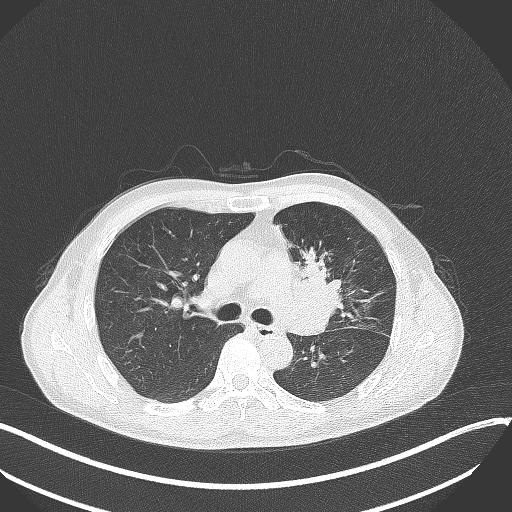
Chest CT, one axial slice. Slice 211 of 411 in the series (ordered by position). Reconstruction kernel B70f. 120 kVp. Lung window (W 1500 / L -600 HU). 1 mm slice thickness. 512 × 512 image matrix, field of view 400 × 400 mm. Male patient, age 56 years. From the clinical record (not read from this slice): clinical TNM (as recorded): T2a N0 M0.
Annotated regions visible in this slice (bounding box drawn by a radiologist):
- lung tumour (recorded histology: squamous cell carcinoma): bounding box (x1, y1, x2, y2) in pixels: (291, 244, 351, 327)